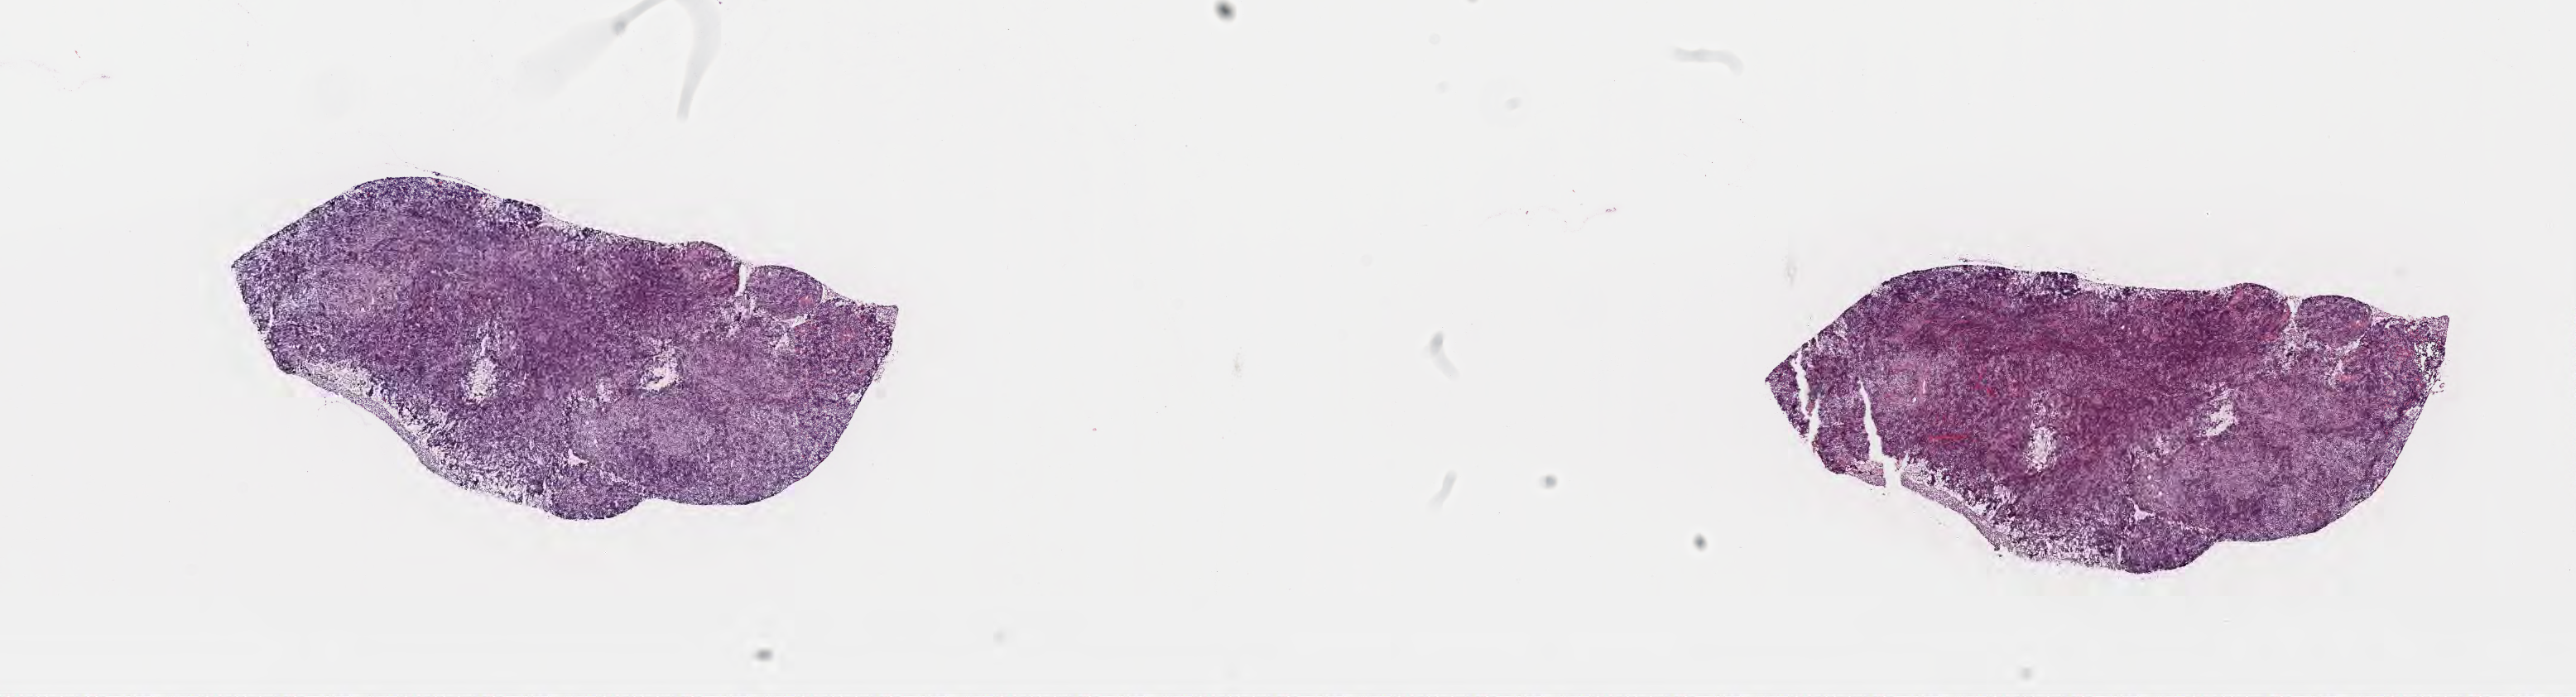
H&E whole-slide image, low-resolution overview of the scanned area, about 25.1 x 6.8 mm; cryosection; primary tumor; site: cranium. Patient: male, age at initial diagnosis 8 years.
Histologic diagnosis: Burkitt lymphoma, NOS.